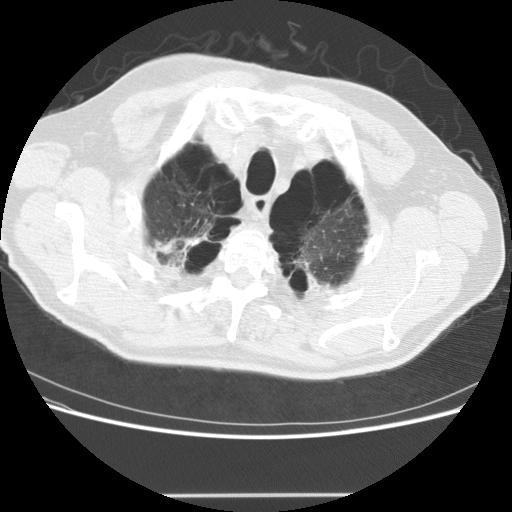
Chest CT (low-dose screening protocol), one axial image; third annual screen; lung window (W 1500 / L -600 HU); 2.5 mm slice thickness; standard (soft-tissue) reconstruction kernel (STANDARD). Male, age 68 years at enrolment.
Expert-annotated lung lesion, box from (x=132, y=213) to (x=217, y=285) px. The screening reader recorded 2 non-calcified nodules or masses ≥4 mm on this exam (lingula, left lower lobe); which of them this box marks is not recorded. Official screen result: positive, no significant change: stable abnormalities potentially related to lung cancer, unchanged since the prior screening exam.